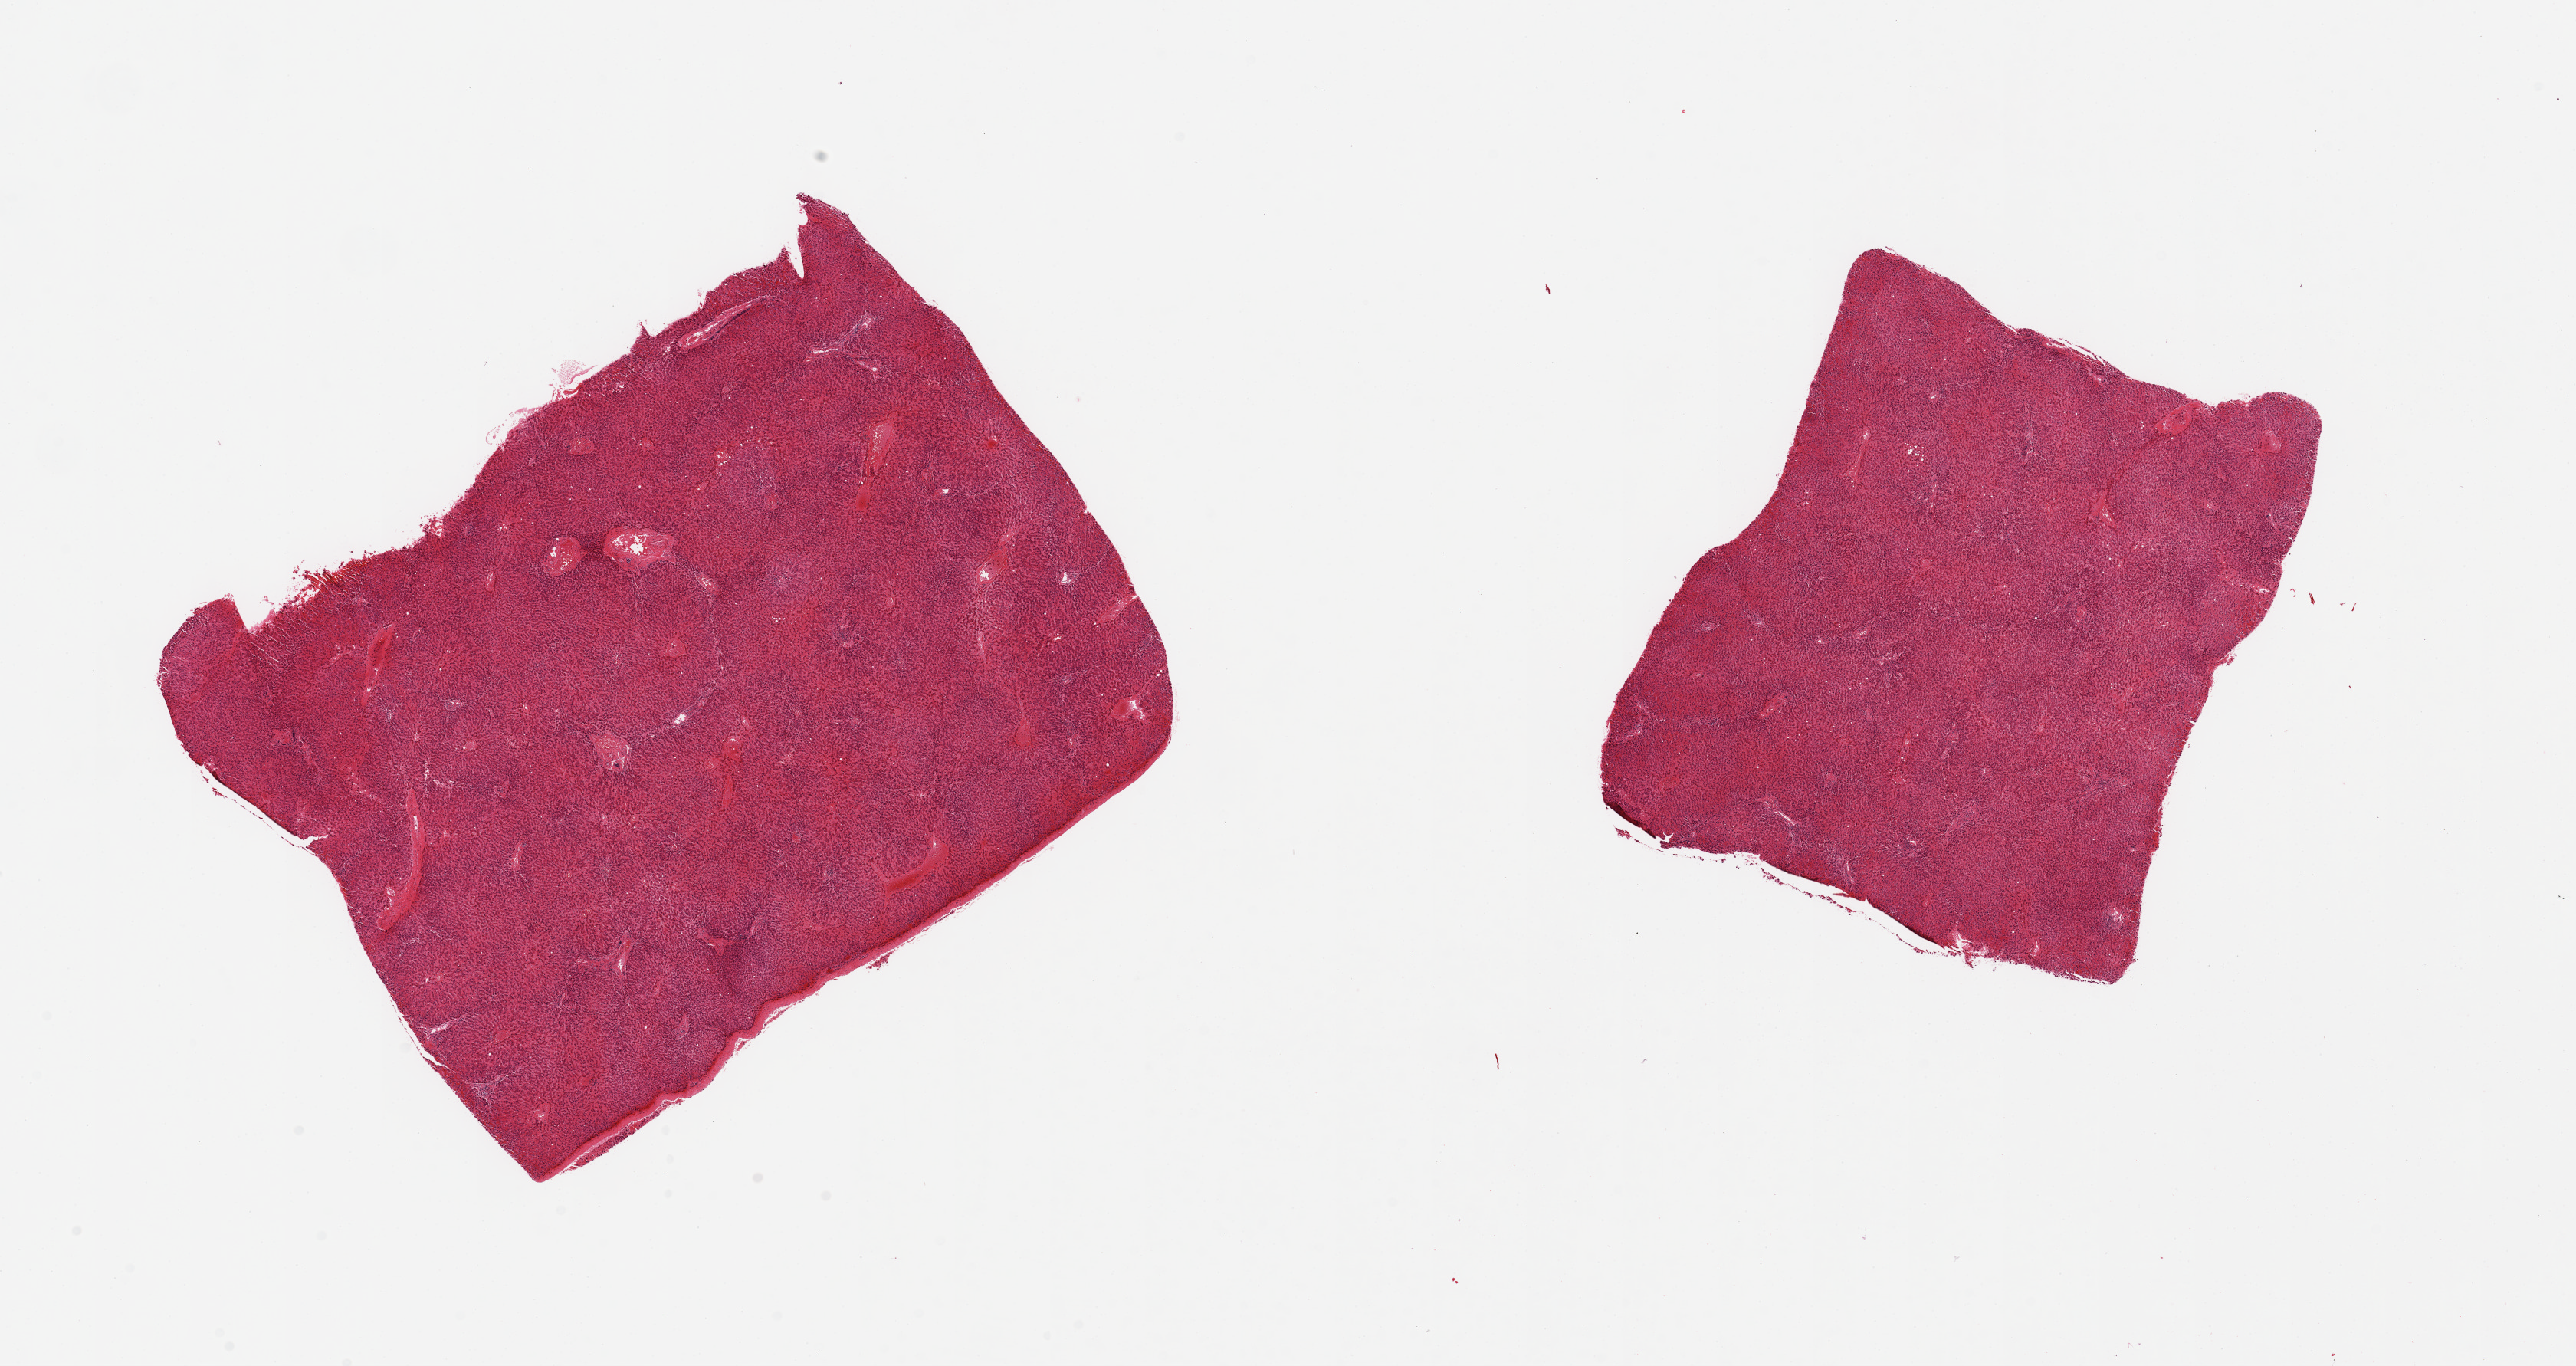
Whole-slide image, haematoxylin and eosin stain — whole scanned area (about 26.6 x 14.1 mm, slide scanned at 20x) shown as a low-resolution overview, PAXgene-fixed paraffin-embedded (PFPE) section, section of liver (target tissue), donor tissue sample. Donor: male.
- pathologist's review note for this sample: 2 pieces; acute vascular congestion